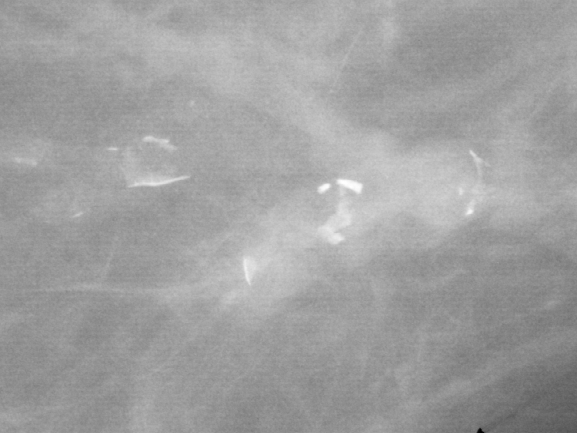
Cropped region of a digitized screen-film mammogram centred on a radiologist-marked abnormality, left breast, CC view.
- Finding: calcifications, morphology eggshell, distribution segmental; BI-RADS assessment category 2; subtlety rating 5 on a 1 (subtle) to 5 (obvious) scale; benign; no additional work-up was recommended (benign without callback).